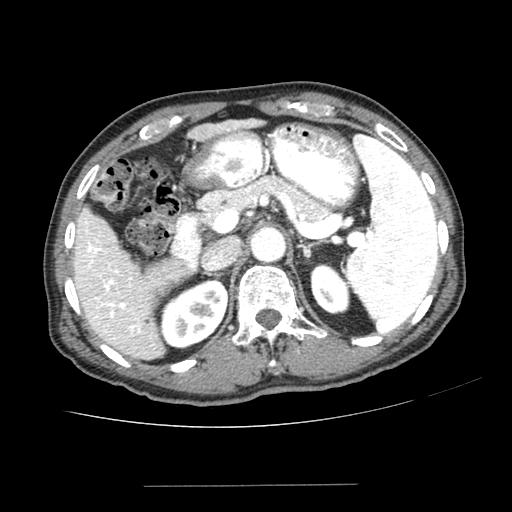
Contrast-enhanced abdominal CT (liver protocol), one axial slice; slice 148 of 187 in the series (ordered by position); one of 2 acquisitions stored at this slice position; soft-tissue window (W 400 / L 40 HU); 512 × 512 image matrix, field of view 360 × 360 mm. Case-level facts recorded for this patient, not image findings: diagnosis: hepatocellular carcinoma (patient treated with transarterial chemoembolisation; whether this scan precedes or follows treatment is not stated here); TNM stage (as recorded): Stage-I; Child-Pugh class: A; tumour differentiation: poorly differentiated; tumour nodularity: uninodular.
Structures marked on this image (semi-automatically segmented with operator editing):
- liver parenchyma outside the tumour (the mass and vessels are separate outlines, so this box may not span the whole liver): bounding box [x1, y1, x2, y2] px = [72, 120, 259, 360]
- liver vessels: [86, 222, 141, 334]